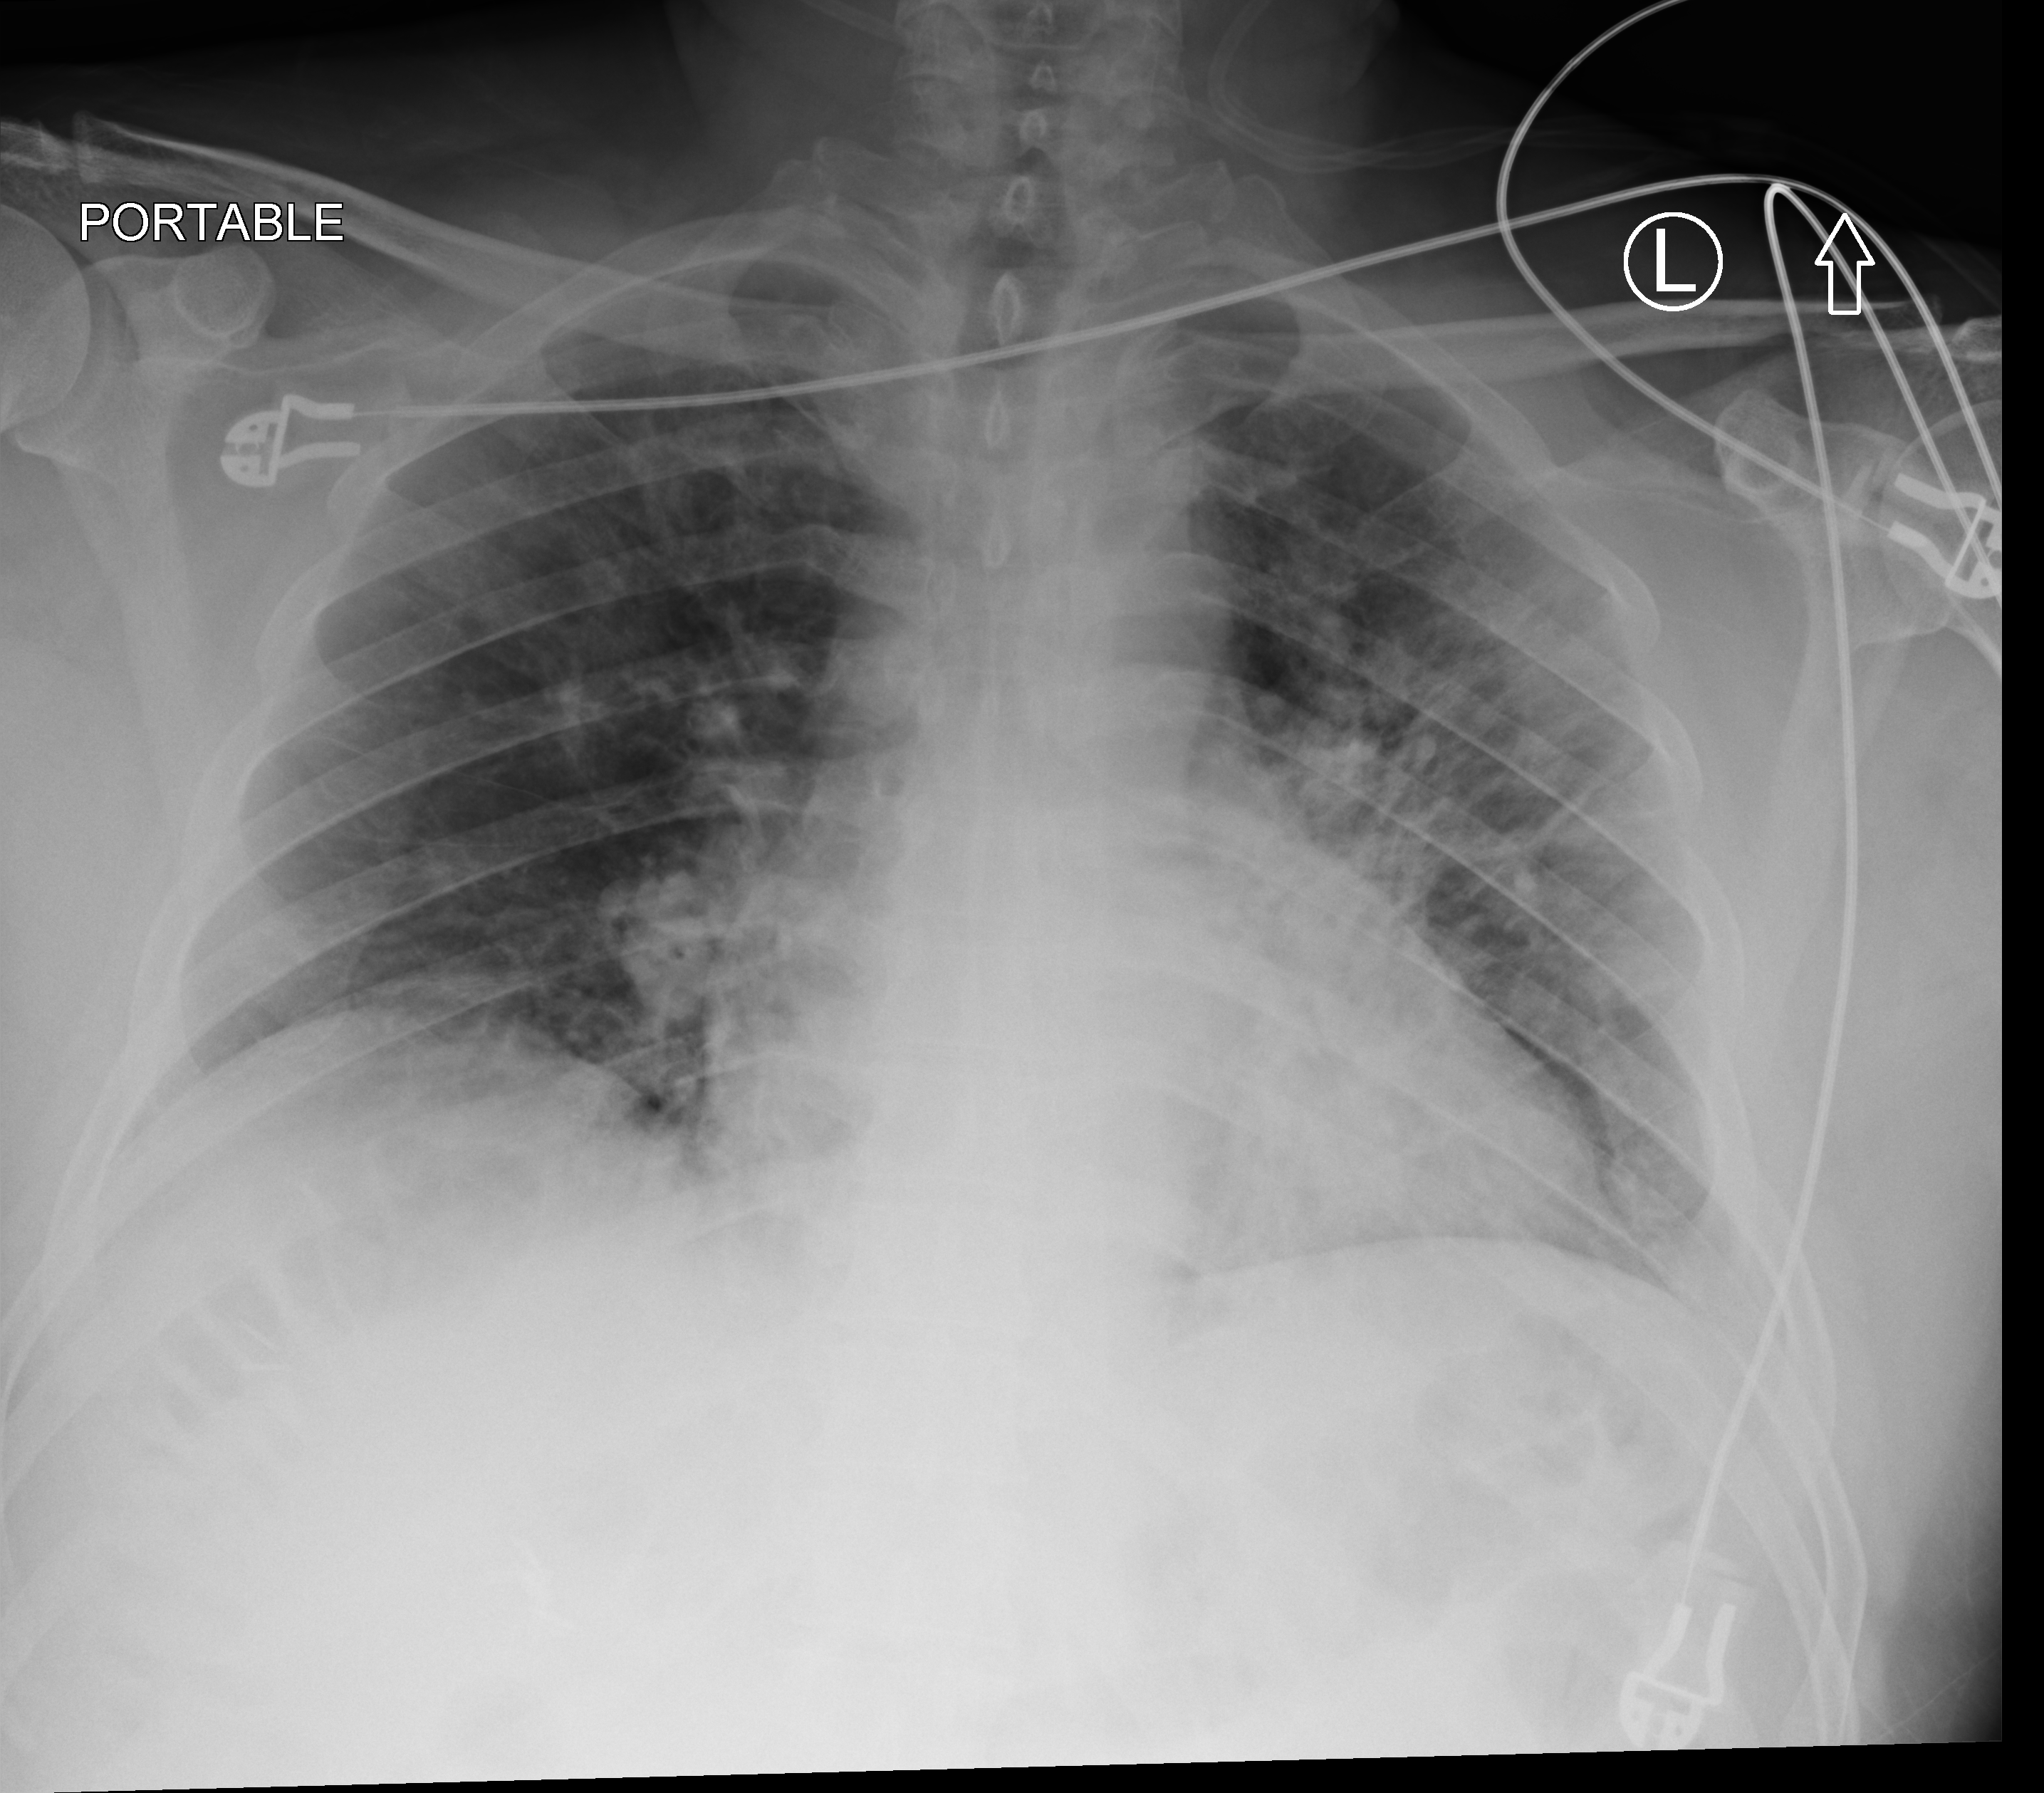
Portable chest radiograph, anteroposterior (AP) projection. Male patient hospitalised with COVID-19, age 18–59 years.
Admission-level facts for this patient (not findings on this image; timing relative to this image not recorded): mechanically ventilated during this hospital stay: no.